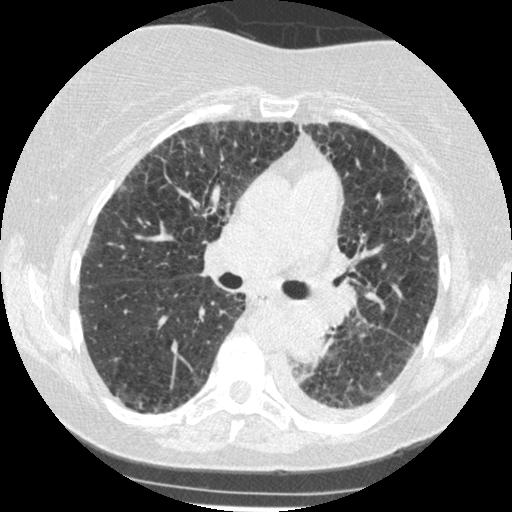
Low-dose screening chest CT, axial slice. Third screening round (two years after baseline). Lung window (W 1500 / L -600 HU). 1.25 mm slice thickness. Slice 188 of 341 in the series. Female participant, aged 60 years at enrolment.
• Lesion marked by an expert reader, bounding box <269,308,341,373> (left, top, right, bottom; pixels).
• Reader record for this screening exam (exam-level; its link to the box is not recorded): non-calcified nodule or mass ≥4 mm, left lower lobe, 54 × 38 mm, smooth margins, soft tissue attenuation, pre-existing on the prior screen: yes; interval growth: yes.
• Official screen result: positive, other.
• Participant outcome: lung cancer diagnosed 15 days after this screen — small cell carcinoma, NOS, left lower lobe, undifferentiated (G4), stage IV (AJCC 6th edition), 69 mm at pathology.